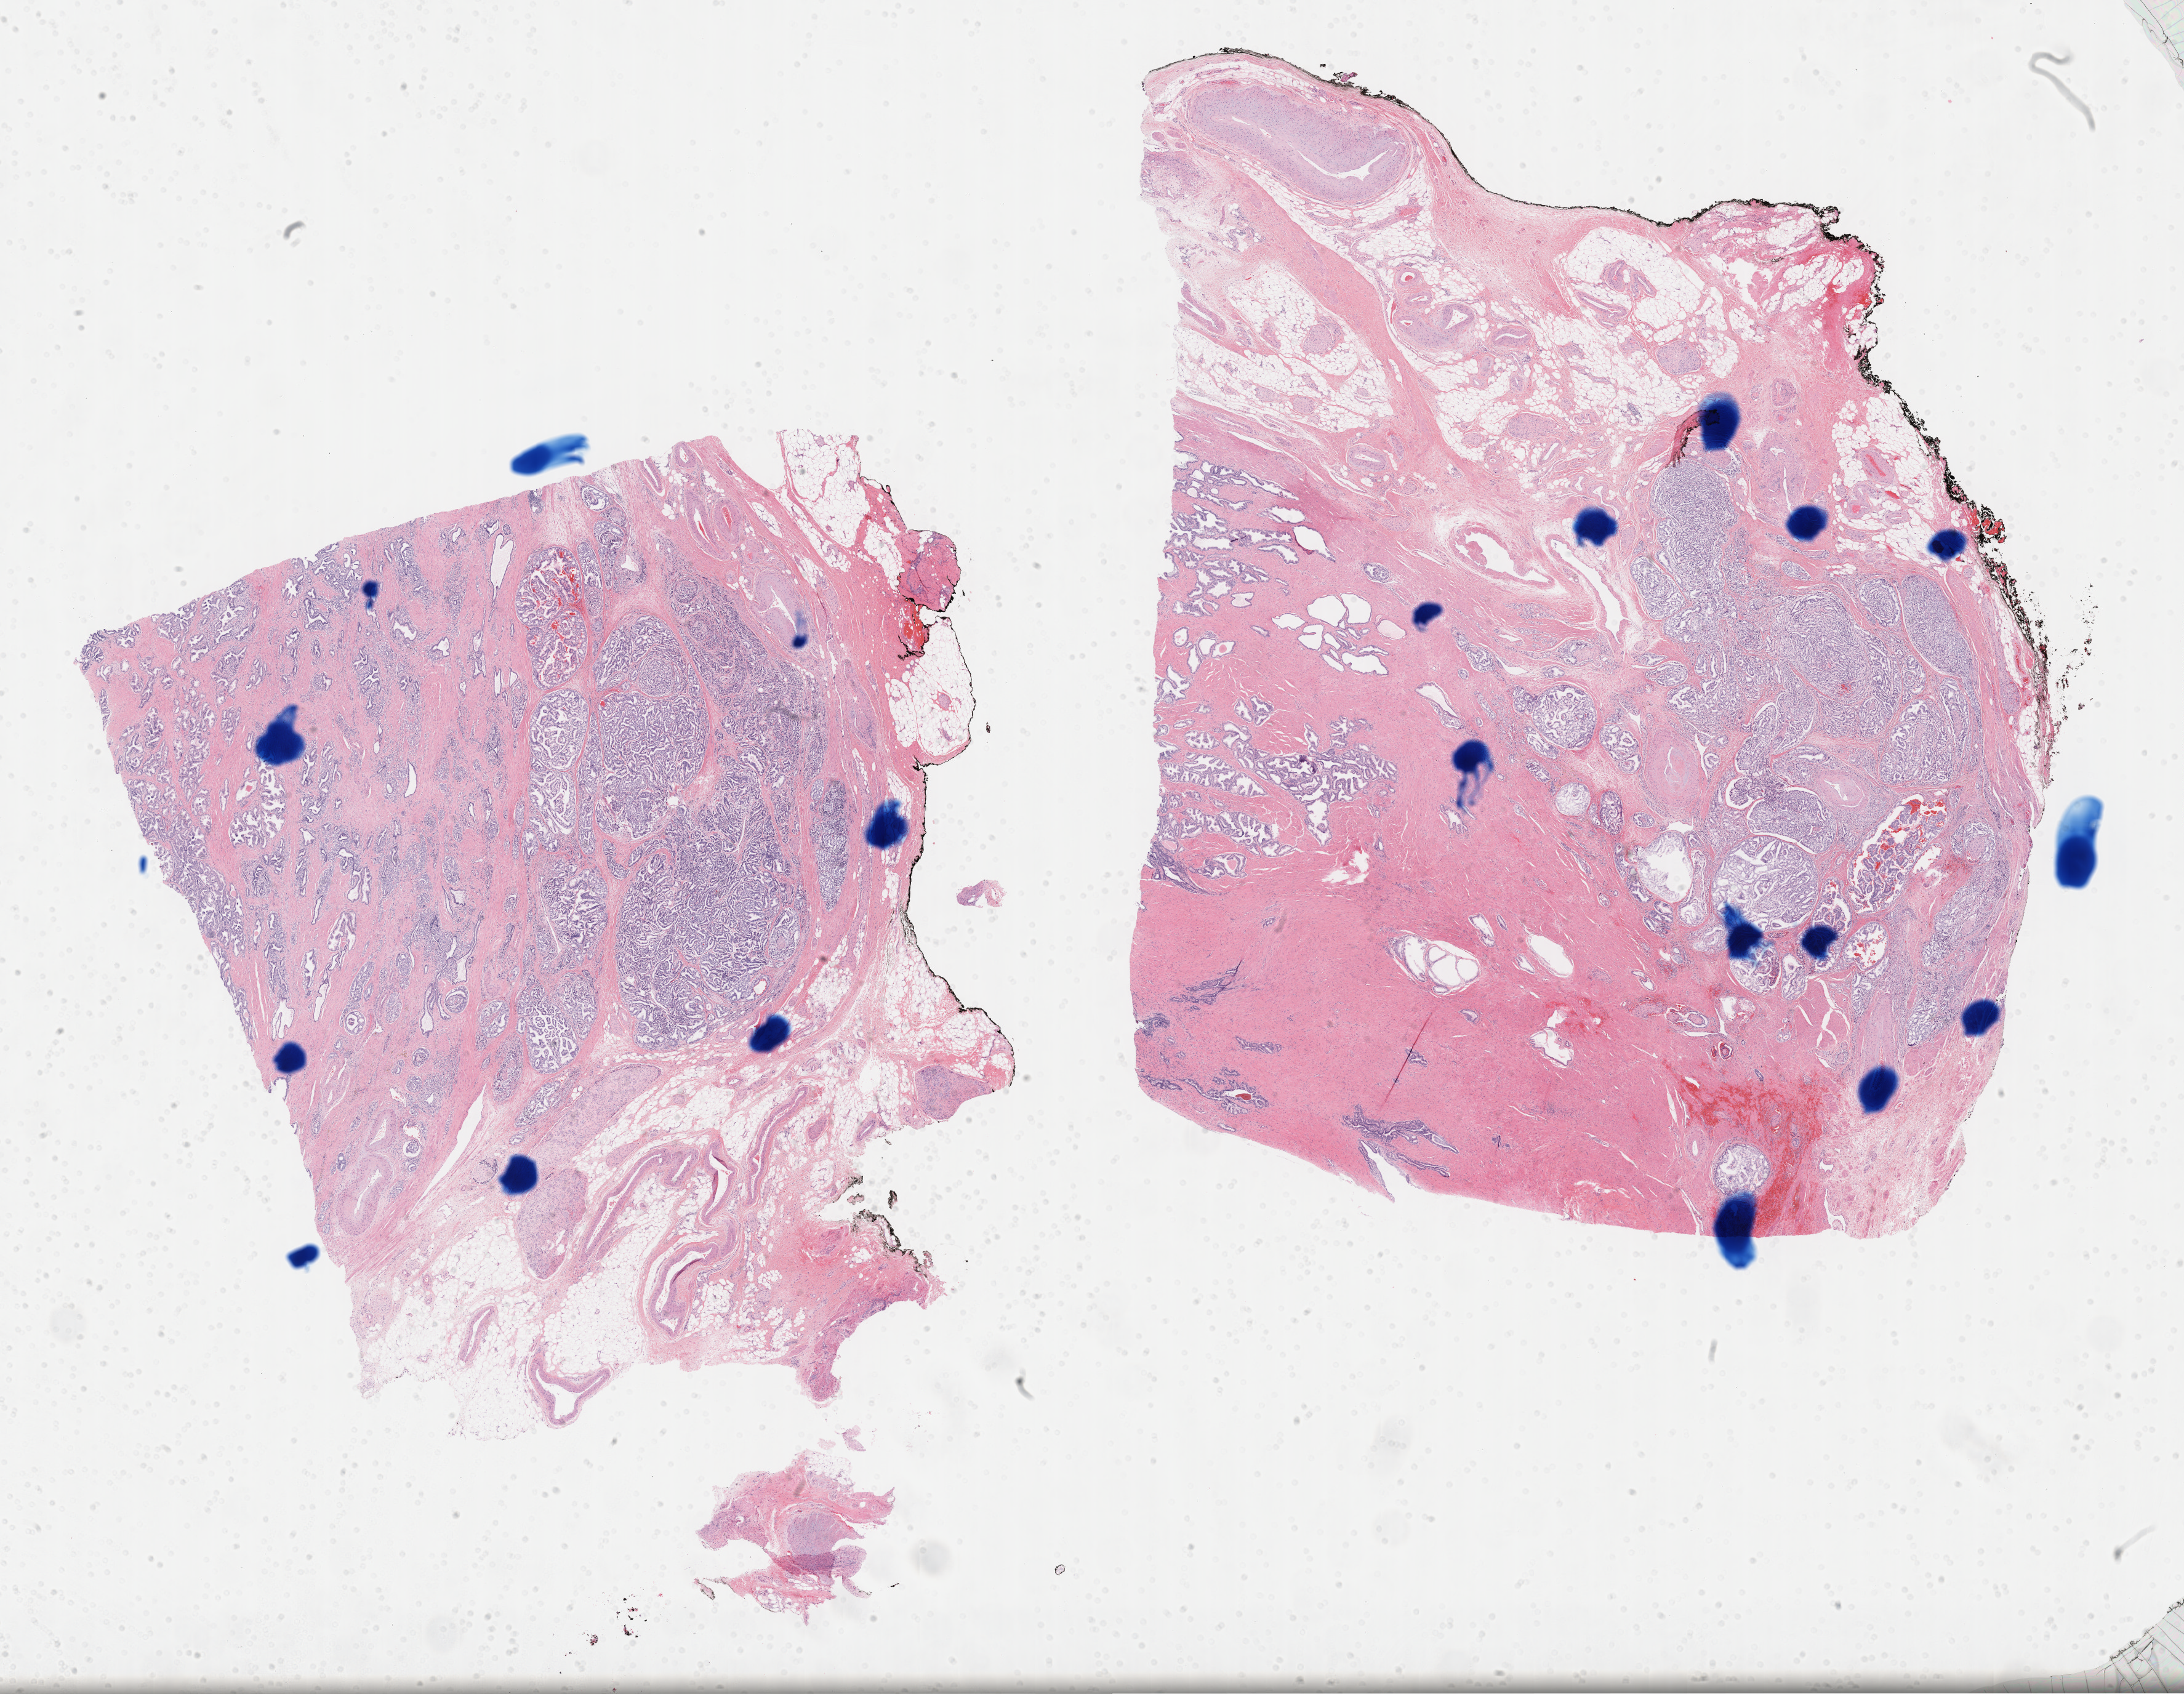
Digitized Hematoxylin and eosin (H&E) stained tissue section (whole slide) — low-resolution overview of the scanned area, about 28.7 x 22.3 mm; formalin-fixed paraffin-embedded (FFPE) diagnostic section; primary tumour sample from the prostate. Patient: male, age at initial diagnosis 52 years. Gleason score: 9 (4+5).
Pathologic diagnosis: Adenocarcinoma, NOS (prostate gland). Laterality: bilateral. Lymph nodes positive (case pathology): 1 of 10 examined.